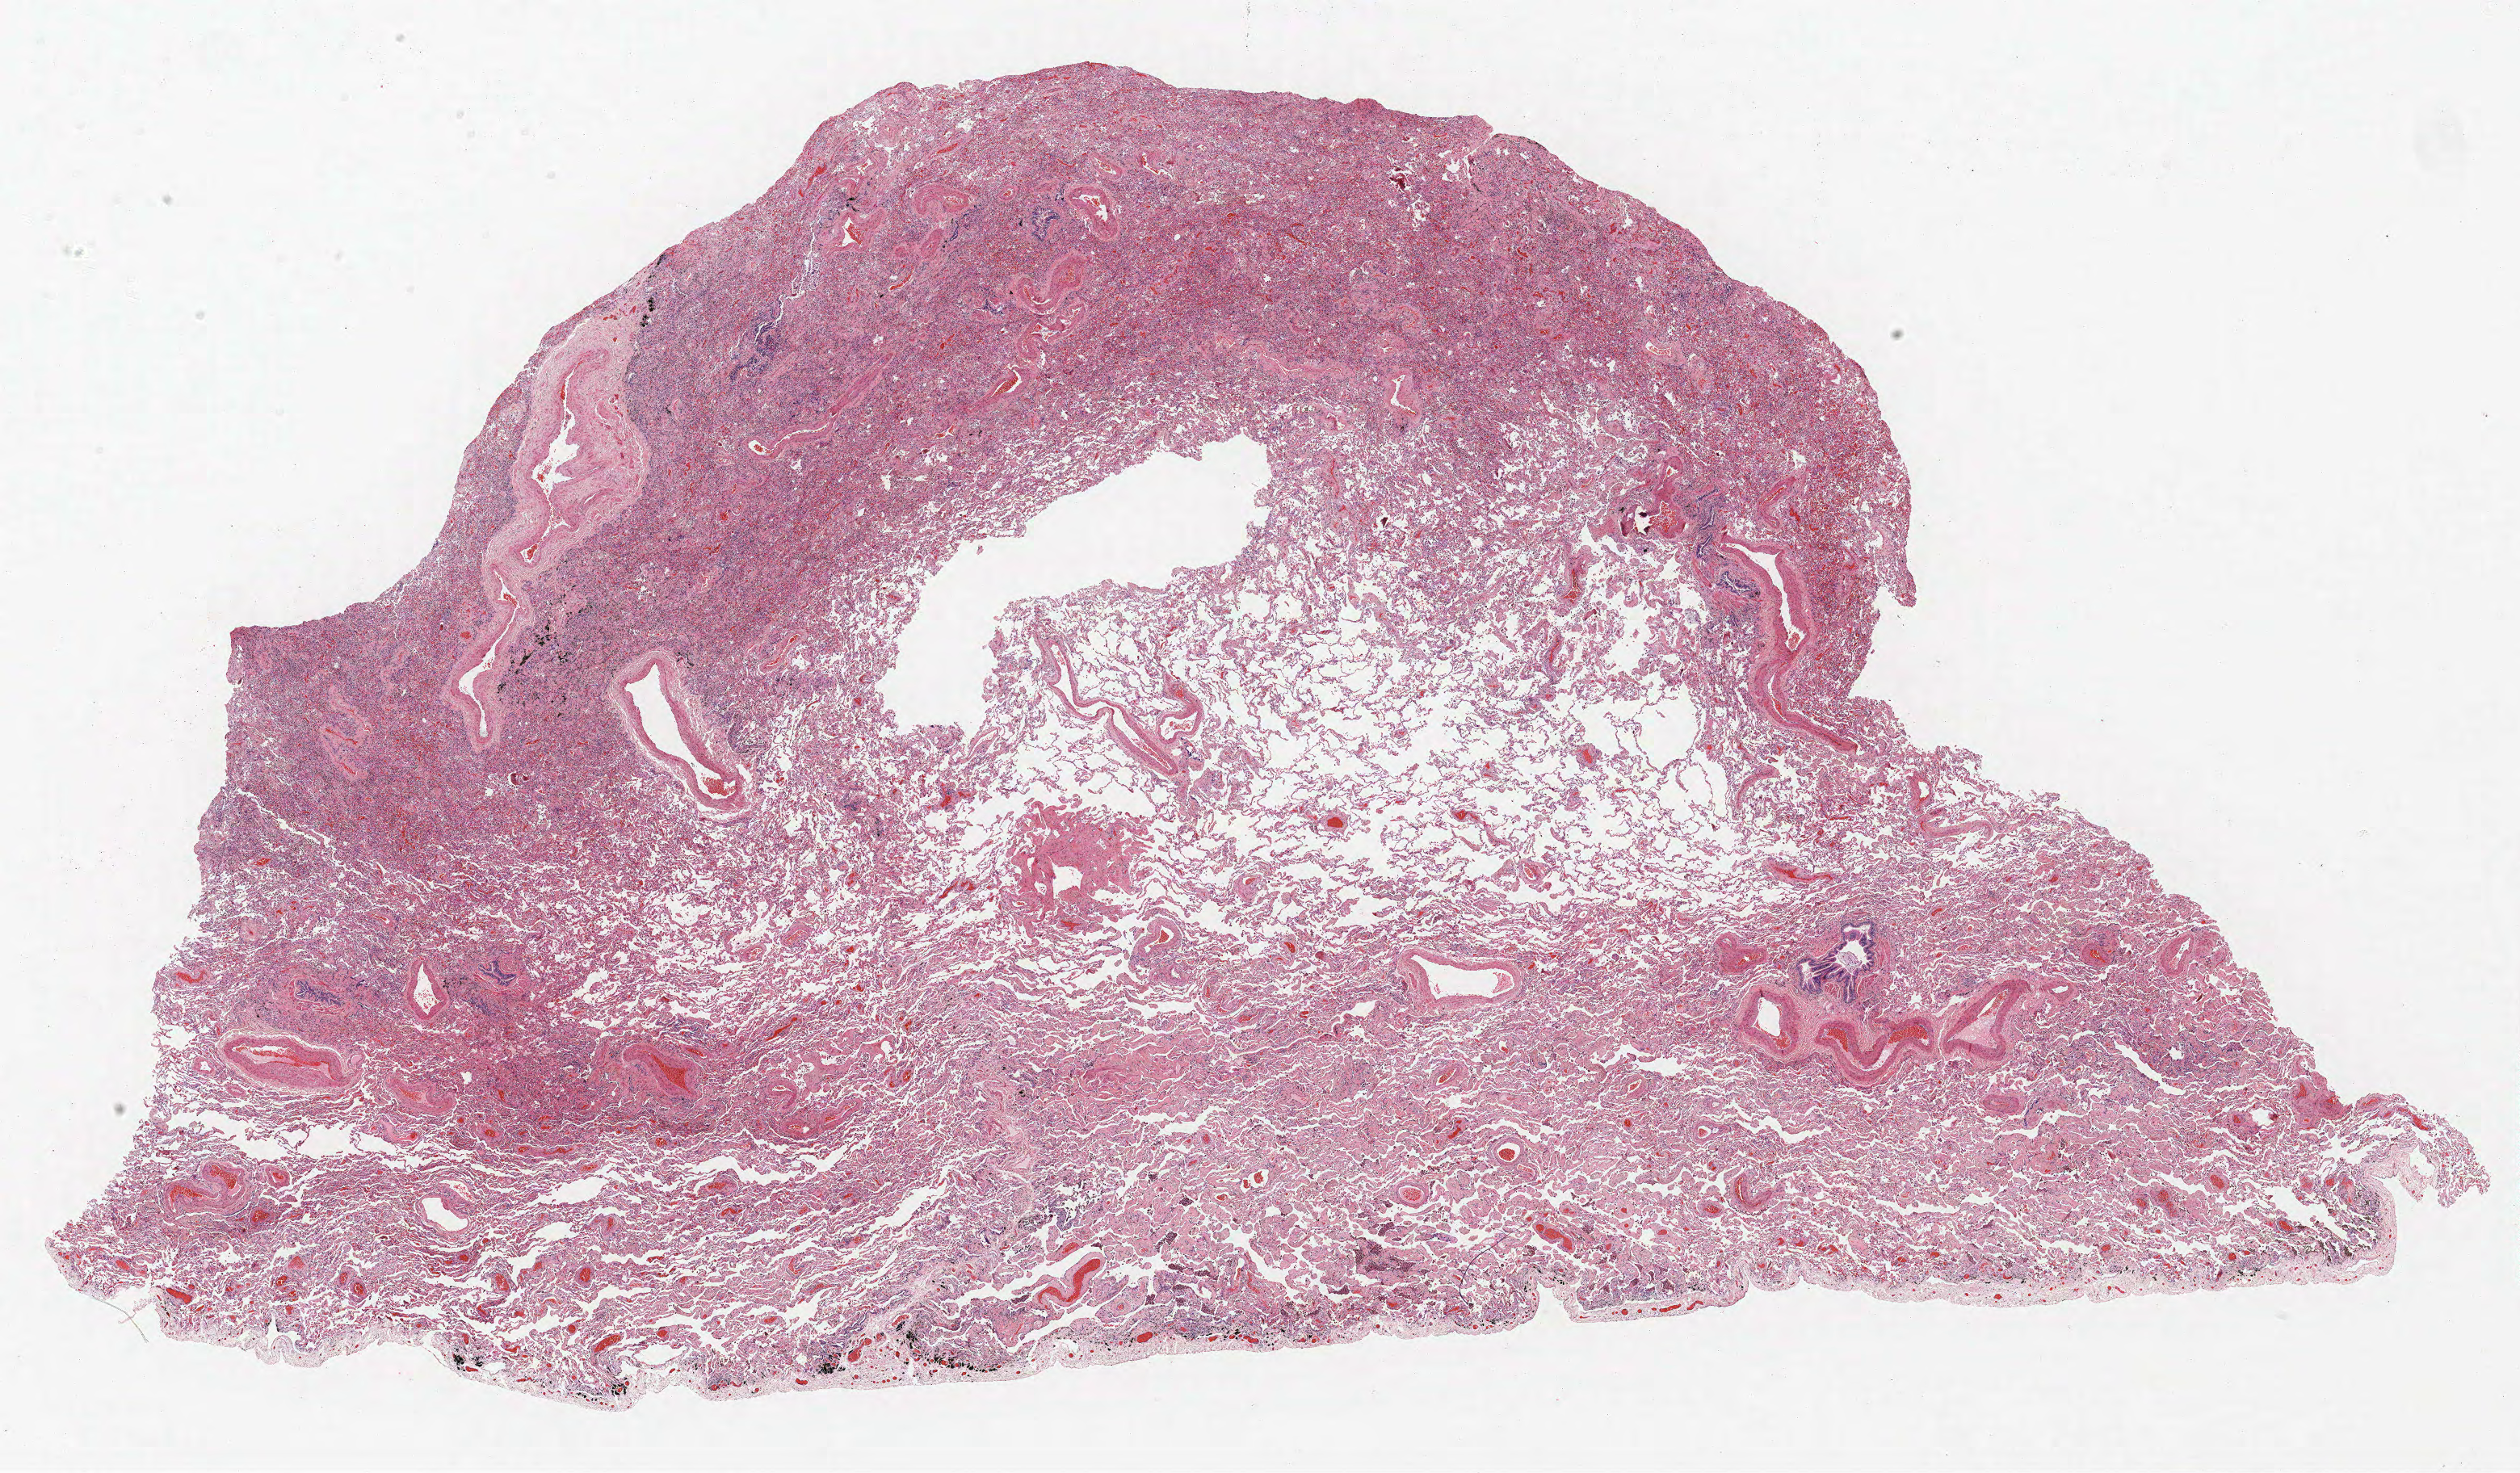
Whole-slide histology image, Hematoxylin and eosin (H&E) stained, shown as a low-resolution overview of the whole scanned area (about 25.0 x 14.6 mm); FFPE section; lung tissue. Male, age 72 at enrolment. Current smoker at enrolment. Grade: moderately differentiated (G2).
Tumour size (pathology): 20 mm. Participant's lung-cancer diagnosis: Squamous cell carcinoma, NOS (ICD-O-3 8070/3). Primary tumour location (clinical record): left upper lobe. Stage (AJCC 6th edition): IA.